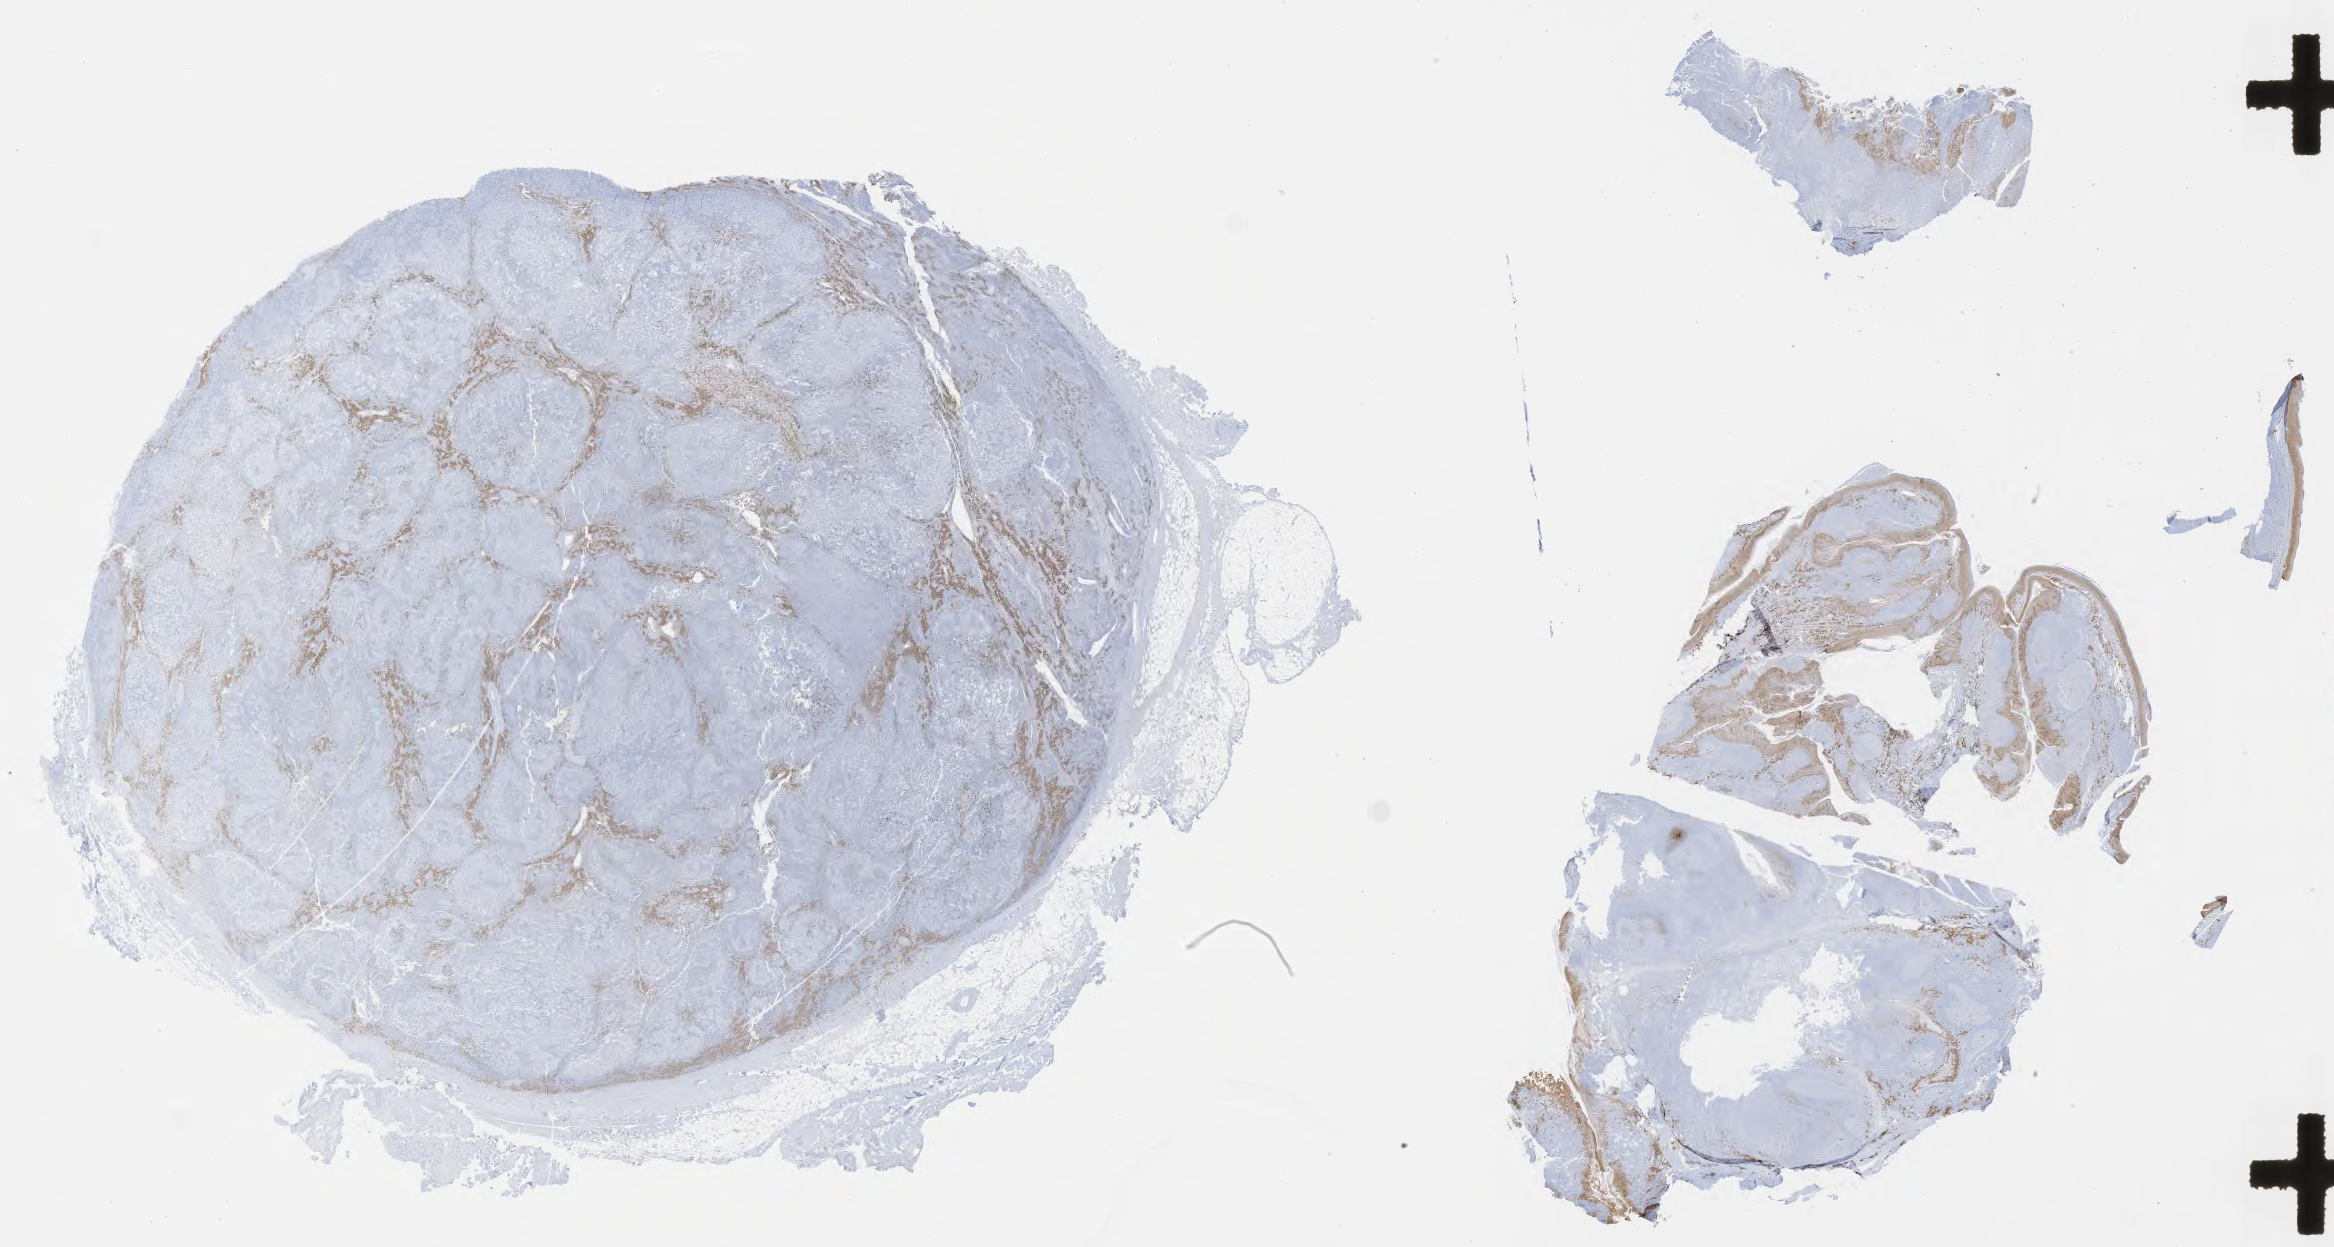
Whole-slide image, immunohistochemical stain for CD138, shown as a low-resolution overview of the whole scanned area (about 37.7 x 20.2 mm), specimen: tumor tissue, site: lymph node. Patient male; aged 46.
* histologic diagnosis: Diffuse large B-cell lymphoma, NOS